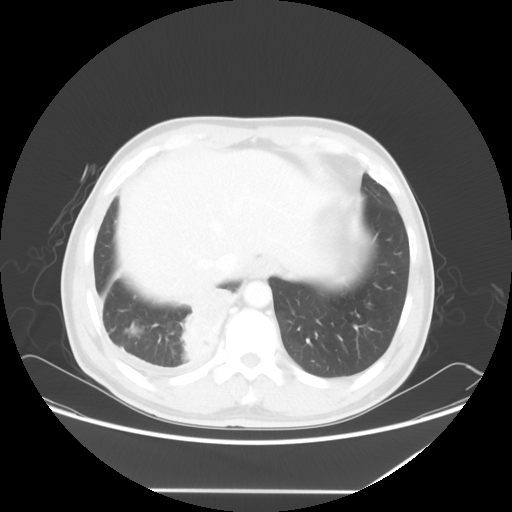
Chest CT, one axial slice. 120 kVp. Lung window (W 1500 / L -600 HU). 5 mm slice thickness. 512 × 512 image matrix, field of view 419 × 419 mm. Male patient, age 48 years. Case-level facts recorded for this patient, not image findings: clinical TNM (as recorded): T3 N3 M1a.
Structures marked on this image (rectangle marked by the reading radiologist):
- lung tumour (recorded histology: squamous cell carcinoma): bounding box (x1, y1, x2, y2) in pixels: (175, 284, 236, 361)